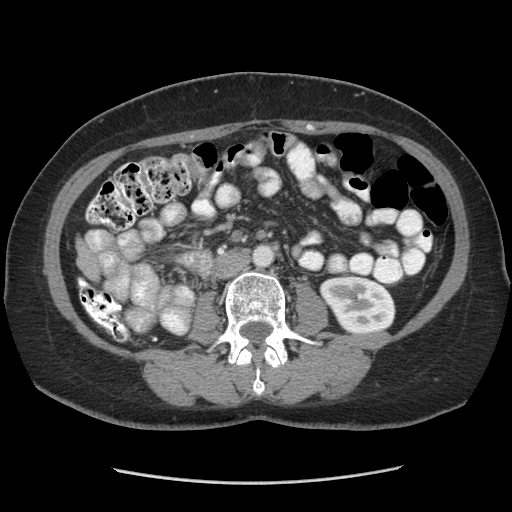
Contrast-enhanced abdominal CT (liver protocol), one axial slice; slice 108 of 185 in the series (ordered by position); 140 kVp; soft-tissue window (W 400 / L 40 HU); 2.5 mm slice thickness; 512 × 512 image matrix. Case-level facts recorded for this patient, not image findings: diagnosis: hepatocellular carcinoma (patient treated with transarterial chemoembolisation; whether this scan precedes or follows treatment is not stated here); TNM stage (as recorded): Stage-I.
Annotated regions visible in this slice (semi-automatic segmentation, software-assisted and operator-edited):
- liver parenchyma outside the tumour (the mass and vessels are separate outlines, so this box may not span the whole liver): bounding box <78,241,82,250> (left, top, right, bottom; pixels)